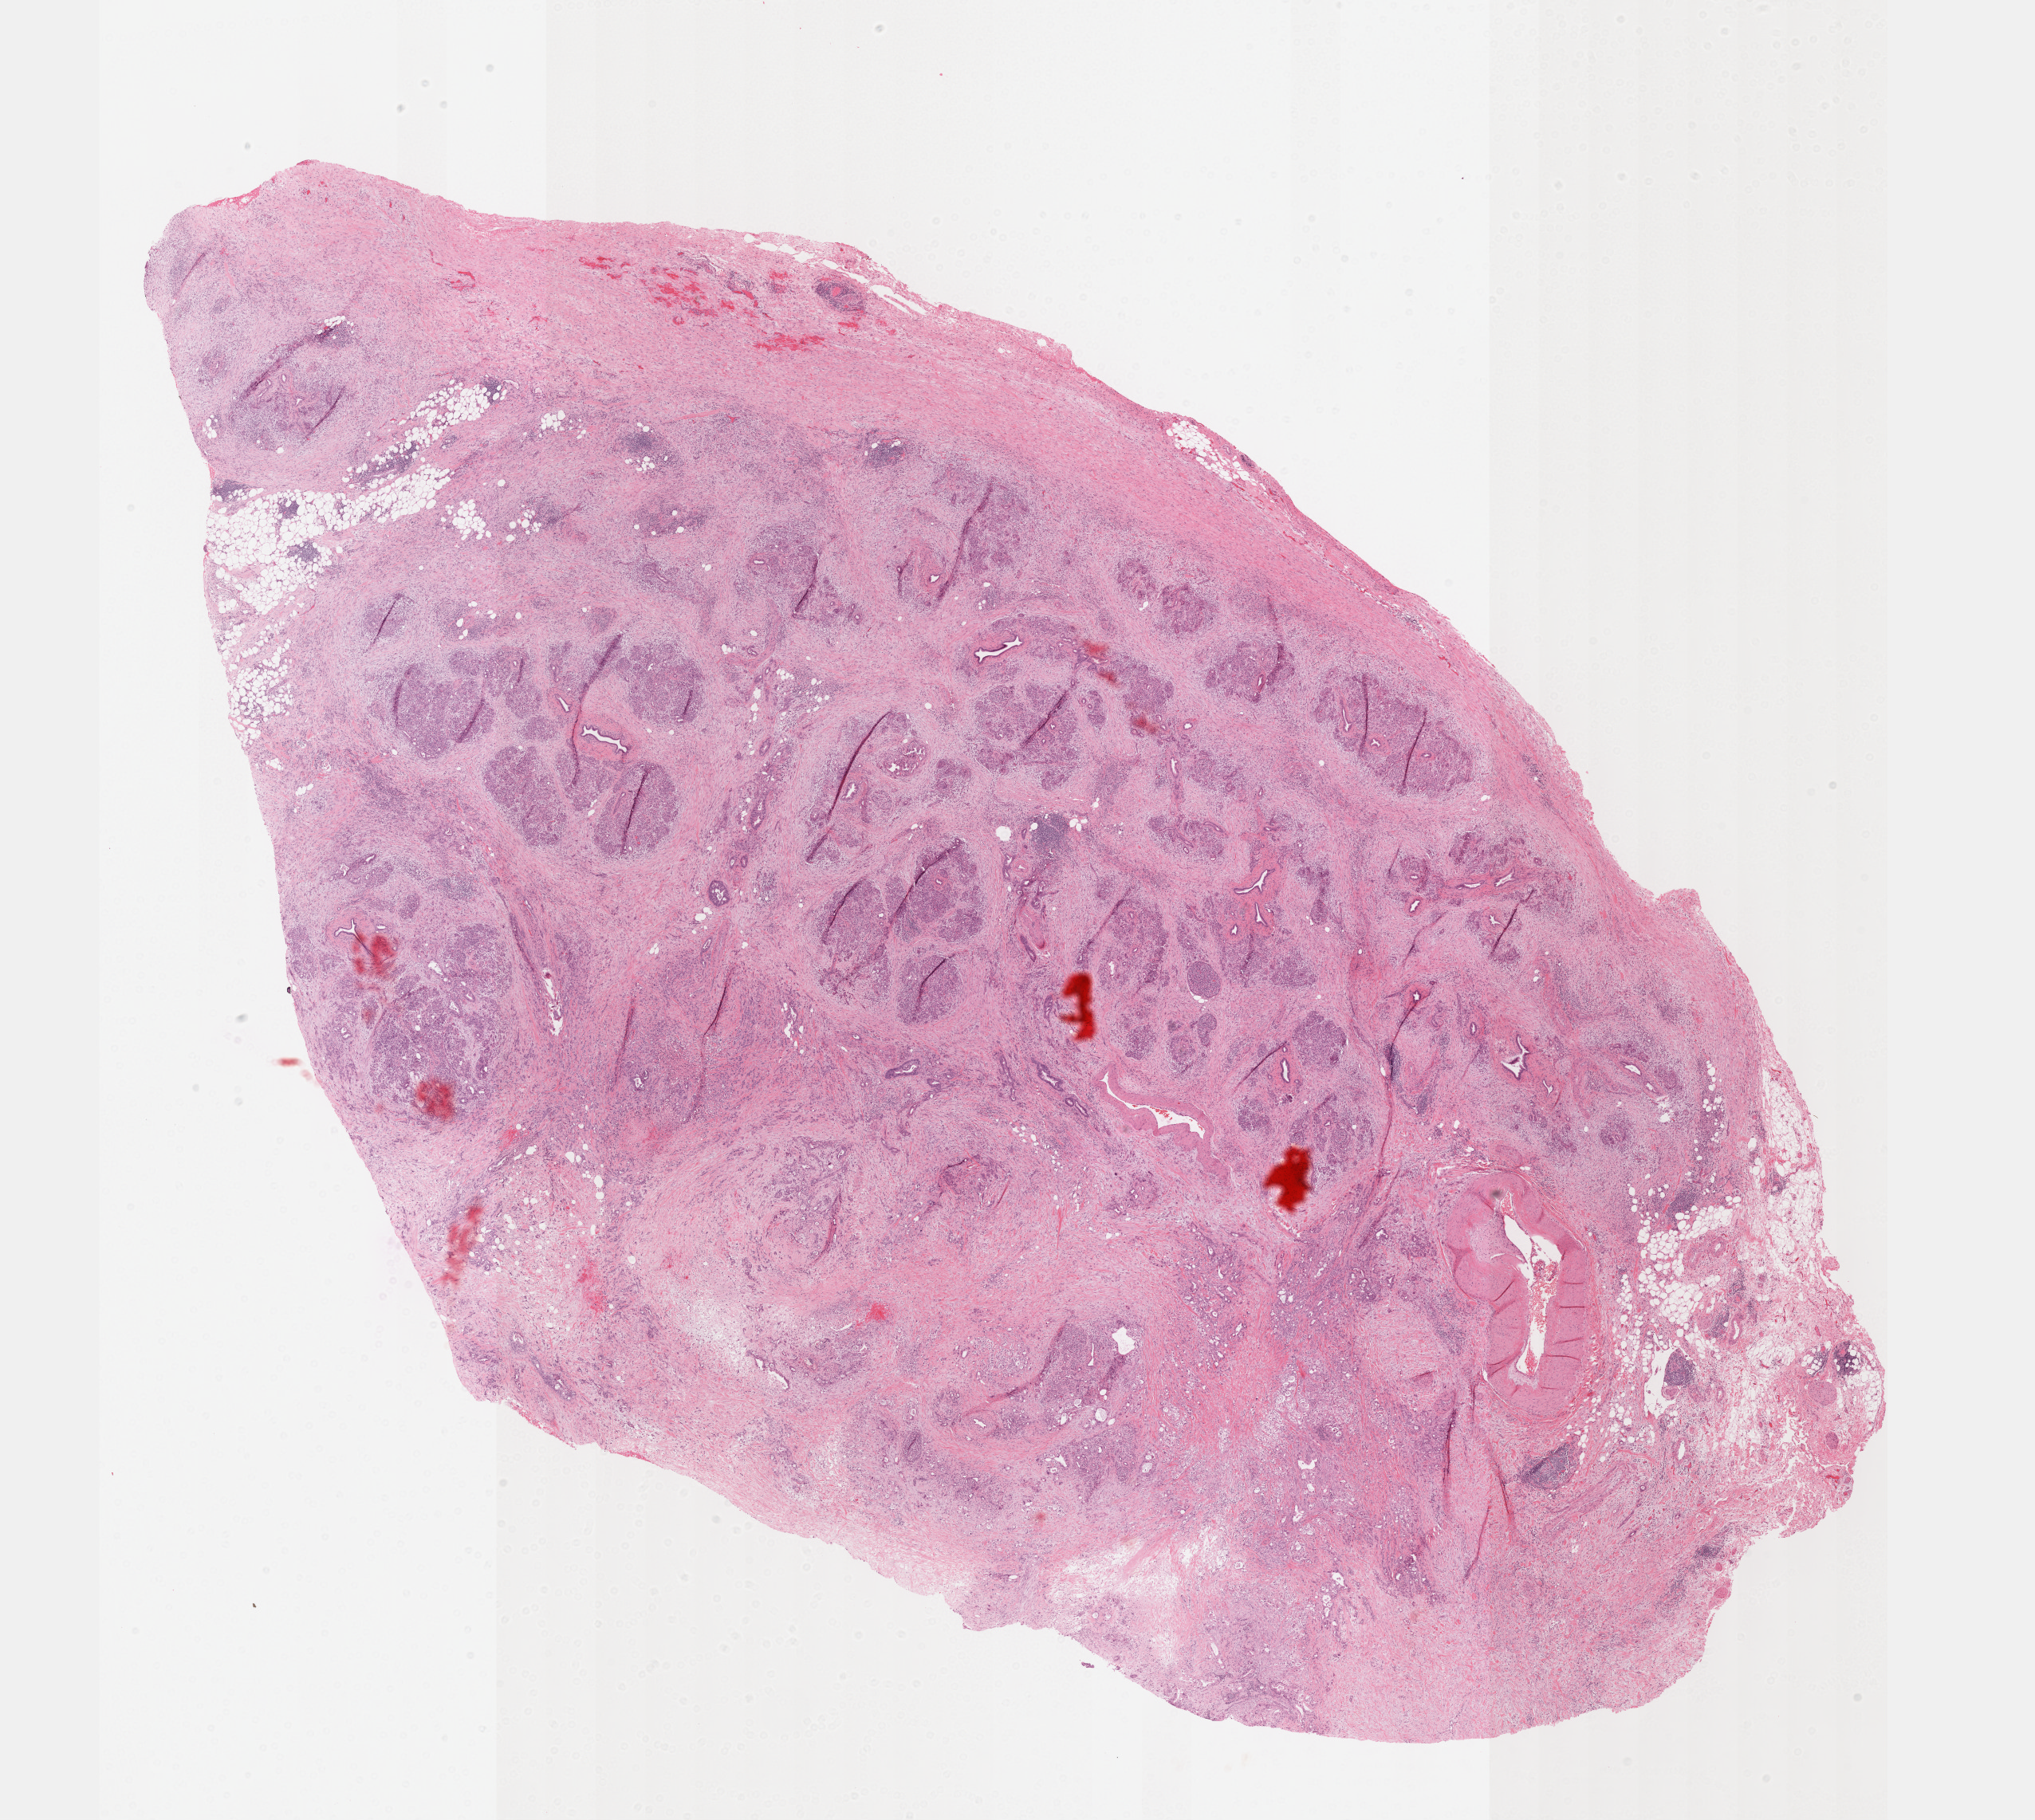
Digitized H&E-stained tissue section (whole slide) — low-resolution overview of the scanned area, about 20.6 x 18.4 mm (acquisition: 40x scan); FFPE section; pancreas, primary tumour sample. Female patient; age at initial diagnosis 72 years.
Diagnosis: Infiltrating duct carcinoma, NOS.